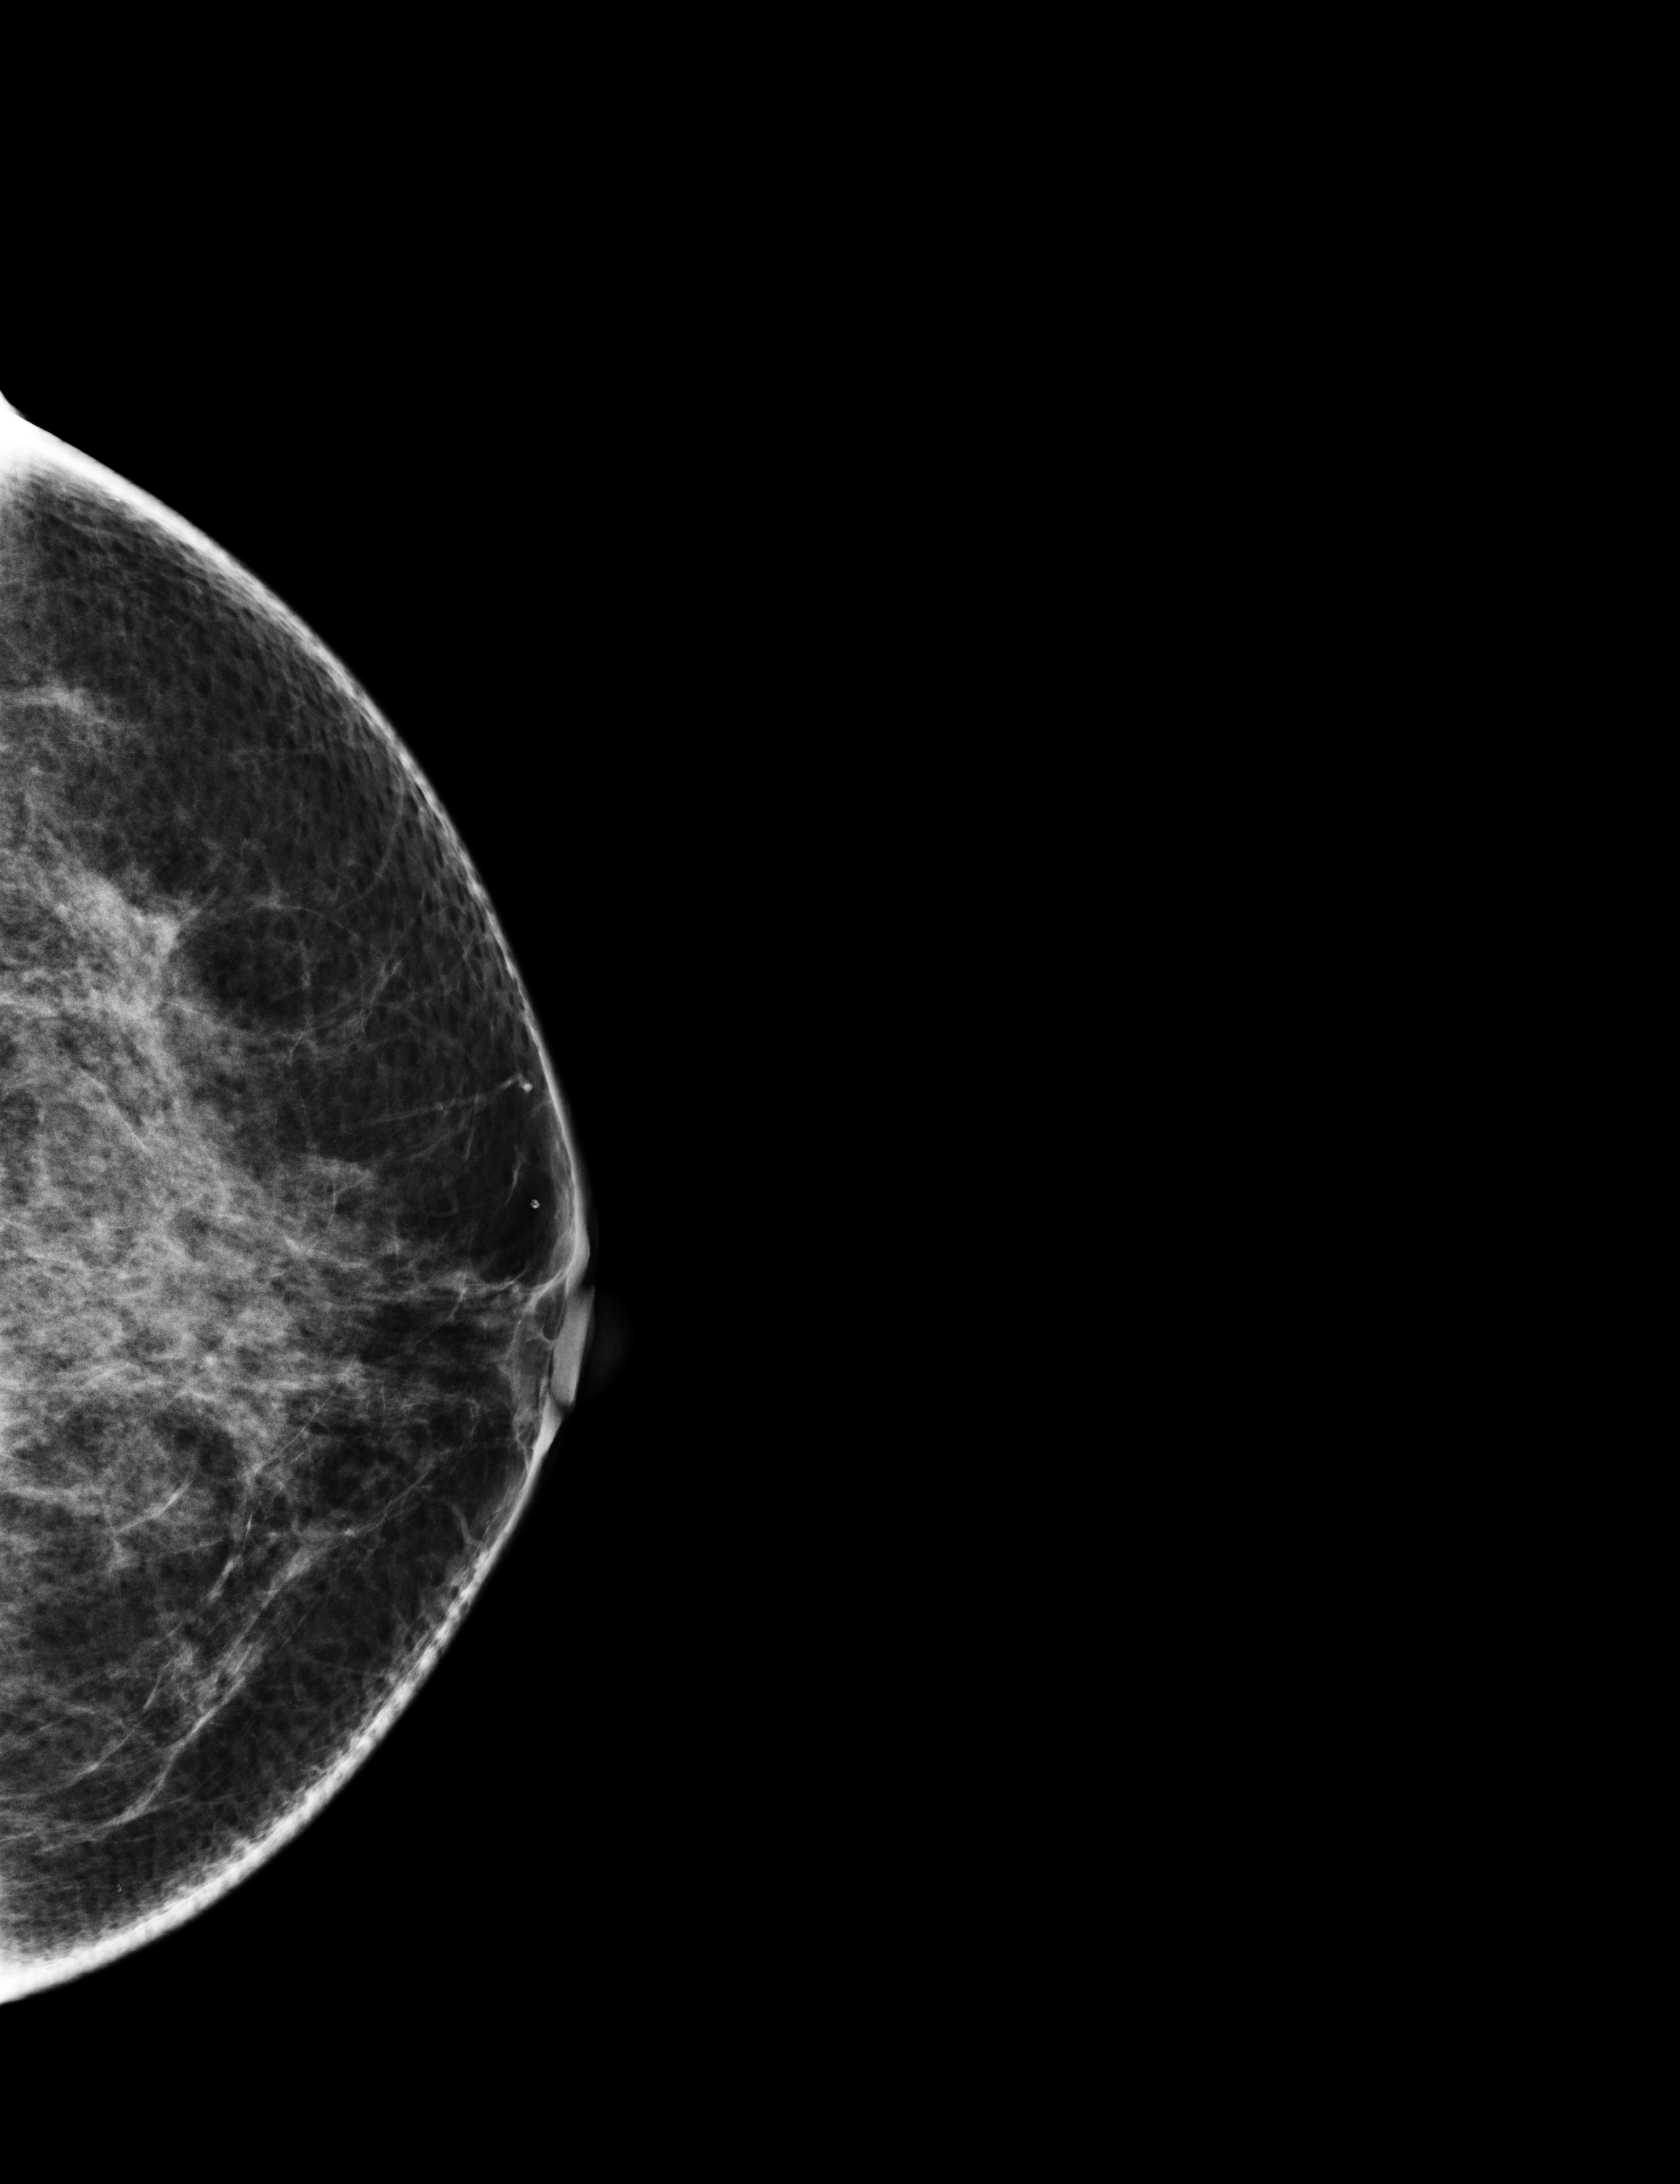
Digital mammogram (FFDM); left breast; cranio-caudal projection; annual screening mammography examination; system: Selenia Dimensions. Female patient, age 43 years.
BI-RADS breast density category at the screening exam (both breasts, scale 1–4): 3. Final BI-RADS assessment for this screening round (tomosynthesis exam, both breasts): category 1. Recall: no recall after this screen.